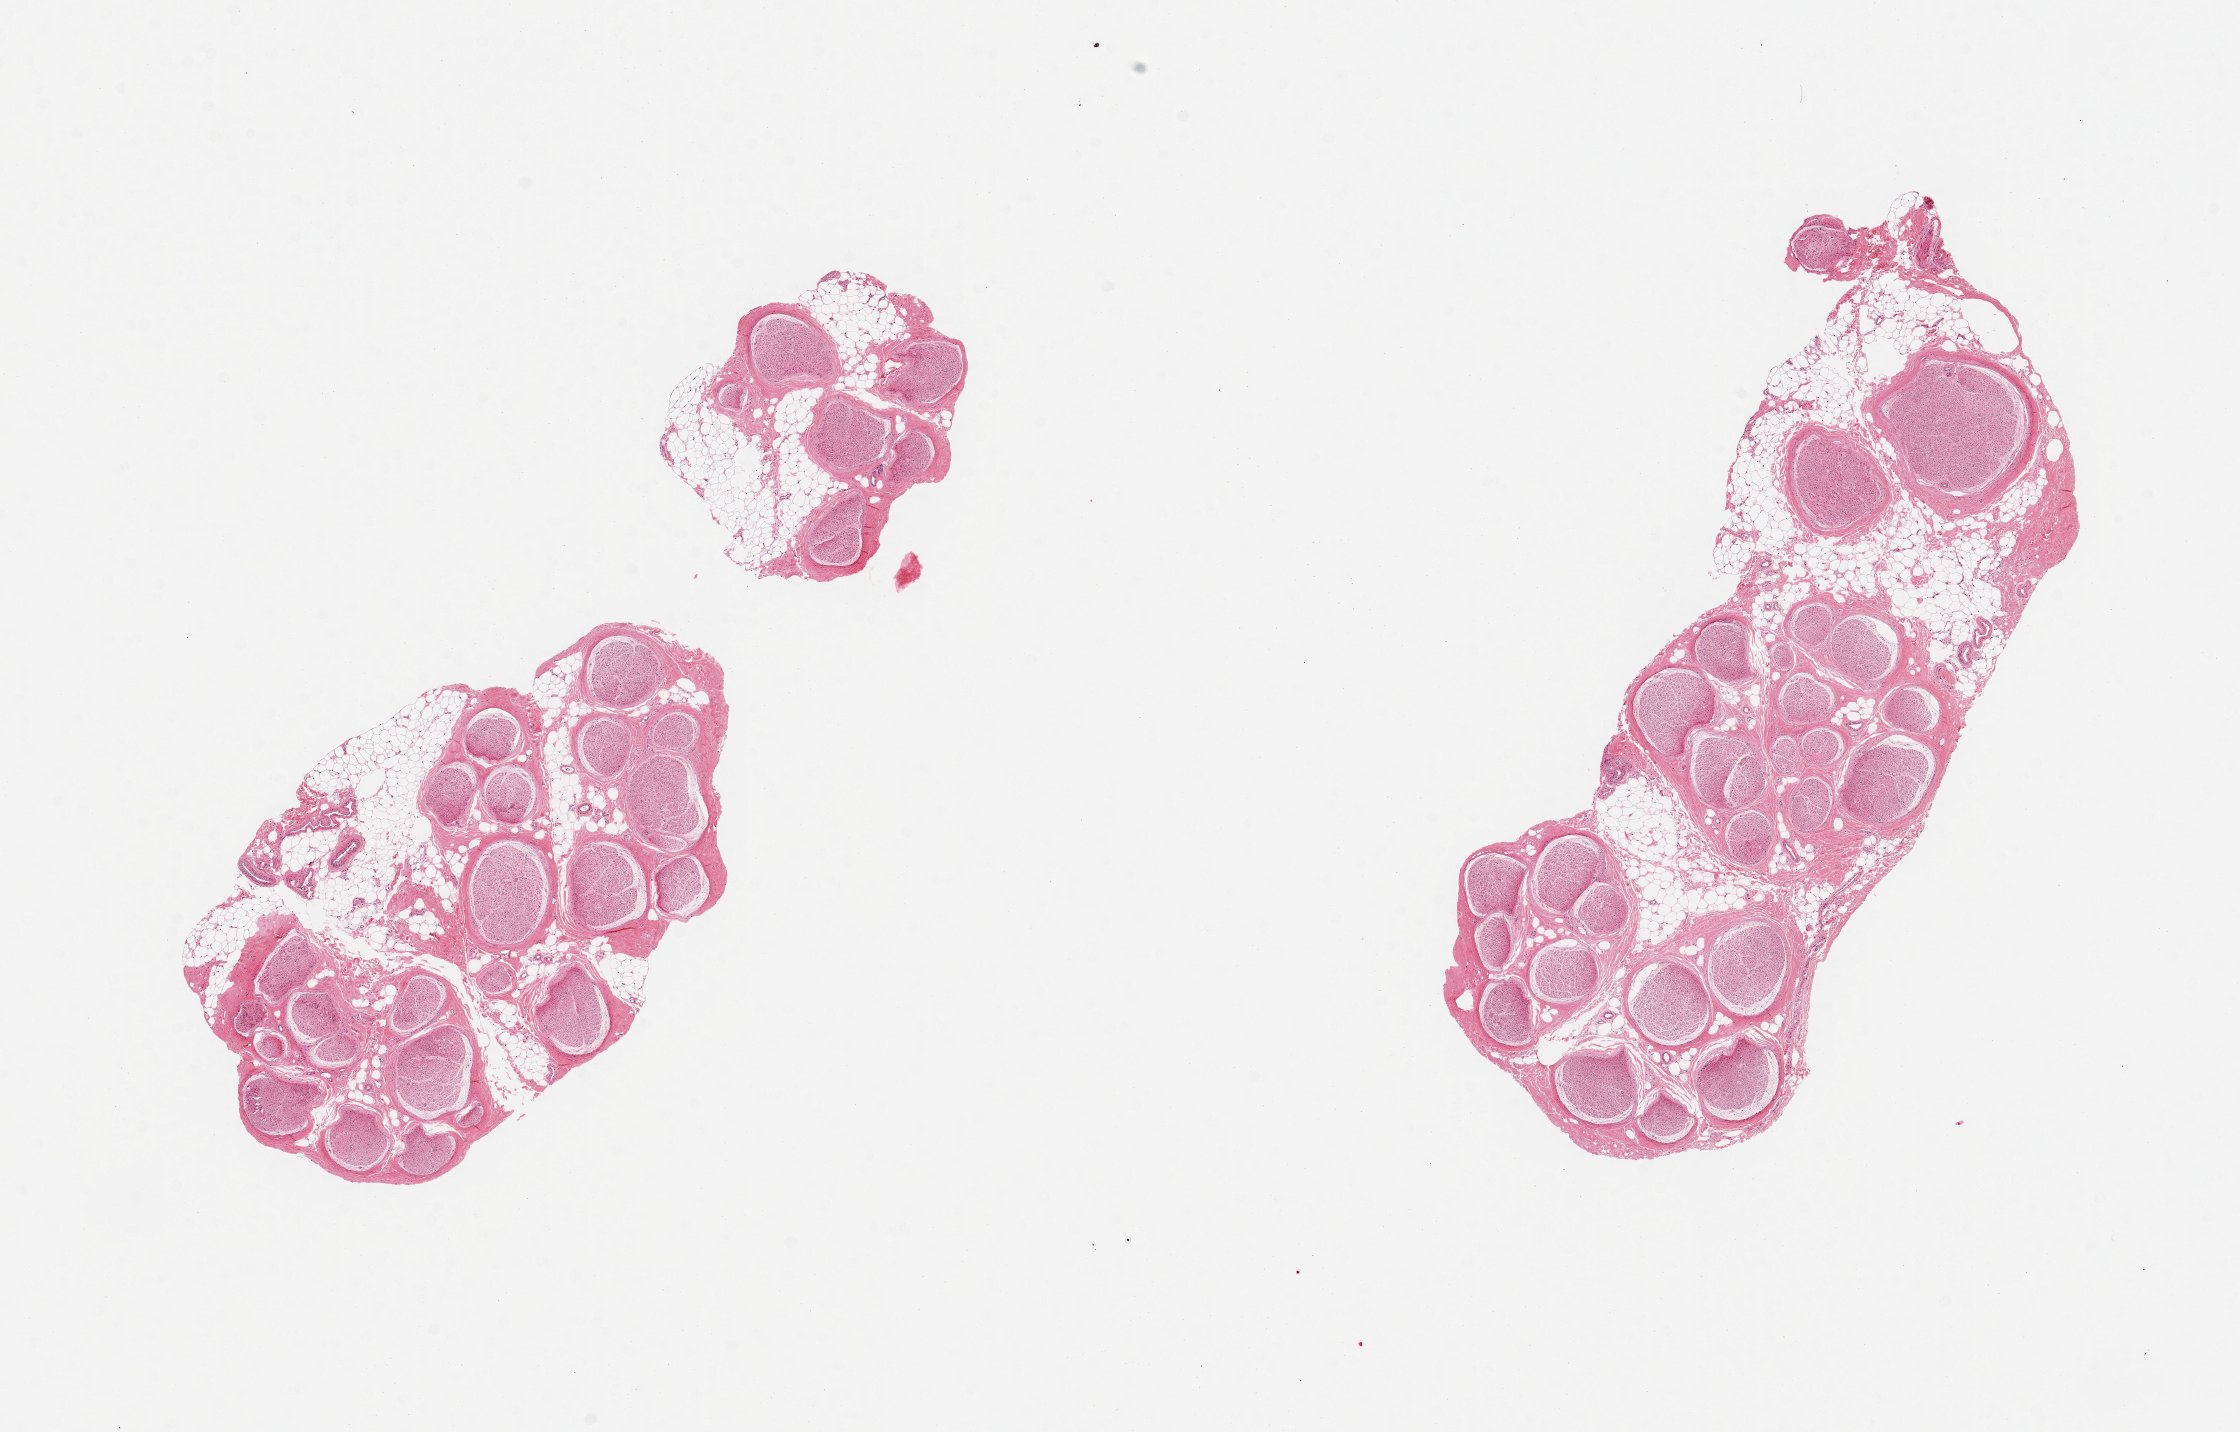
Digitized hematoxylin and eosin (H&E)-stained section, brightfield — a low-resolution overview of the entire scanned area, about 17.7 x 11.3 mm, PAXgene-fixed paraffin-embedded (PFPE) section, section of tibial nerve (target tissue), tissue donor sample.
Review note (as recorded): 2 pieces, trace adherent fat.